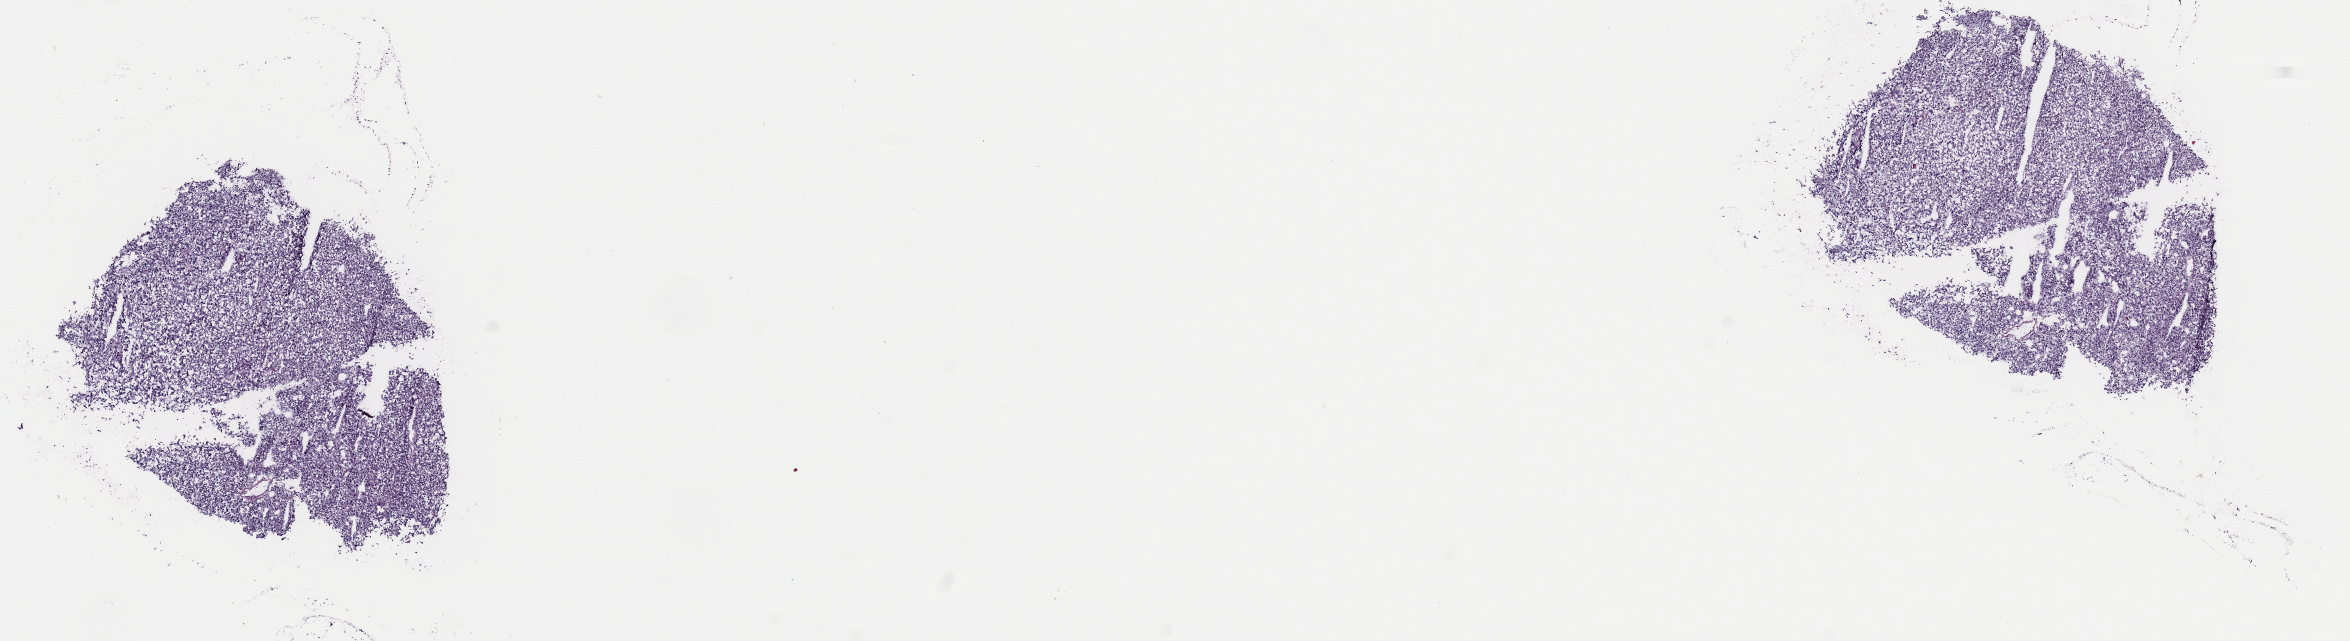
Hematoxylin and eosin (H&E) stained whole-slide image, shown as a low-resolution overview of the whole scanned area (about 18.6 x 5.1 mm, acquisition: 40x scan), frozen section, primary tumour sample from the adrenal gland. Female patient; age at initial diagnosis 43 years. Pathologist review of this section (percent, as recorded): tumour cells 100%, tumour nuclei 80%, normal cells 0%, stromal cells 0%, necrosis 0%. Inflammatory infiltration, as recorded: lymphocyte infiltration 1%, monocyte infiltration 0%, neutrophil infiltration 0%.
Diagnosis: Pheochromocytoma, NOS.